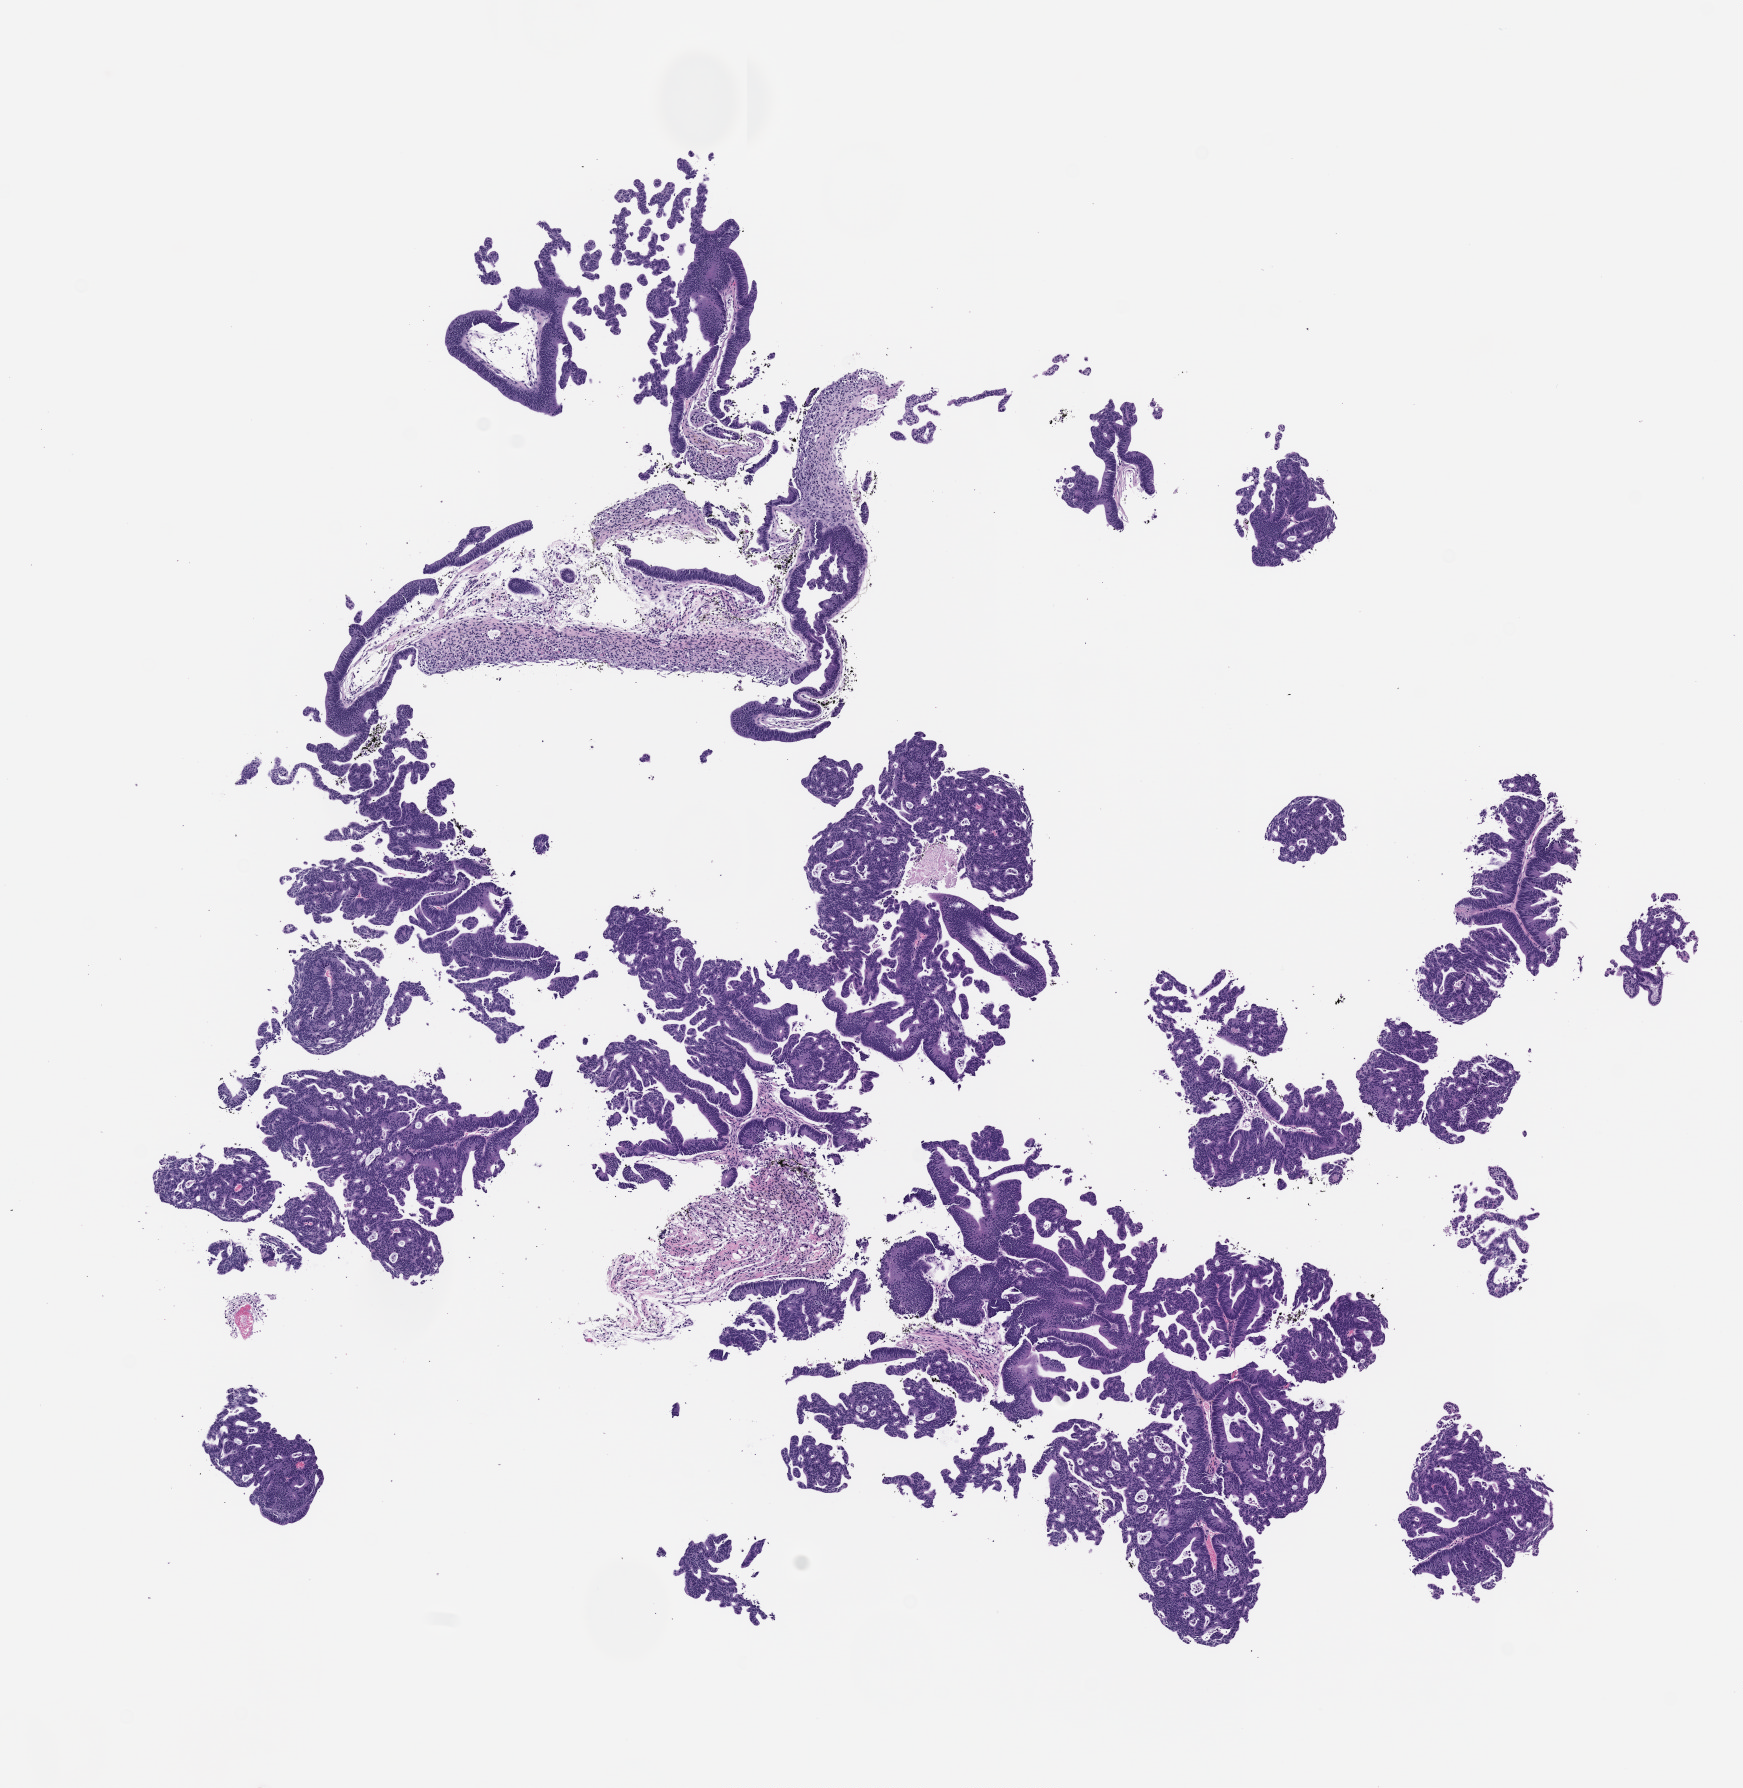
H&E whole-slide image of a patient-derived xenograft (PDX) tumor grown in a mouse, passage 2 — shown as a low-resolution overview of the whole scanned area (about 7.0 x 7.2 mm), formalin-fixed paraffin-embedded section, tumor site category: gastrointestinal tract.
Originating patient diagnosis: Colorectal Carcinoma.